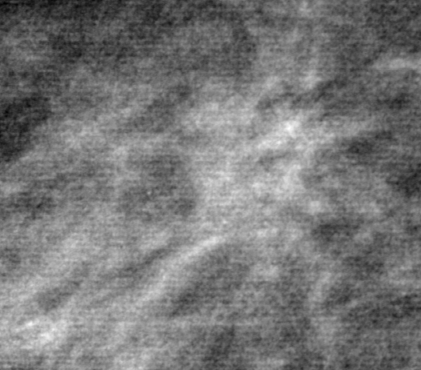
Region of interest cut from a scanned film mammogram (one marked finding); left breast; MLO view.
Mass, shape architectural distortion, margins ill defined; BI-RADS assessment category 4; pathology result (as recorded, not read from the image): benign.